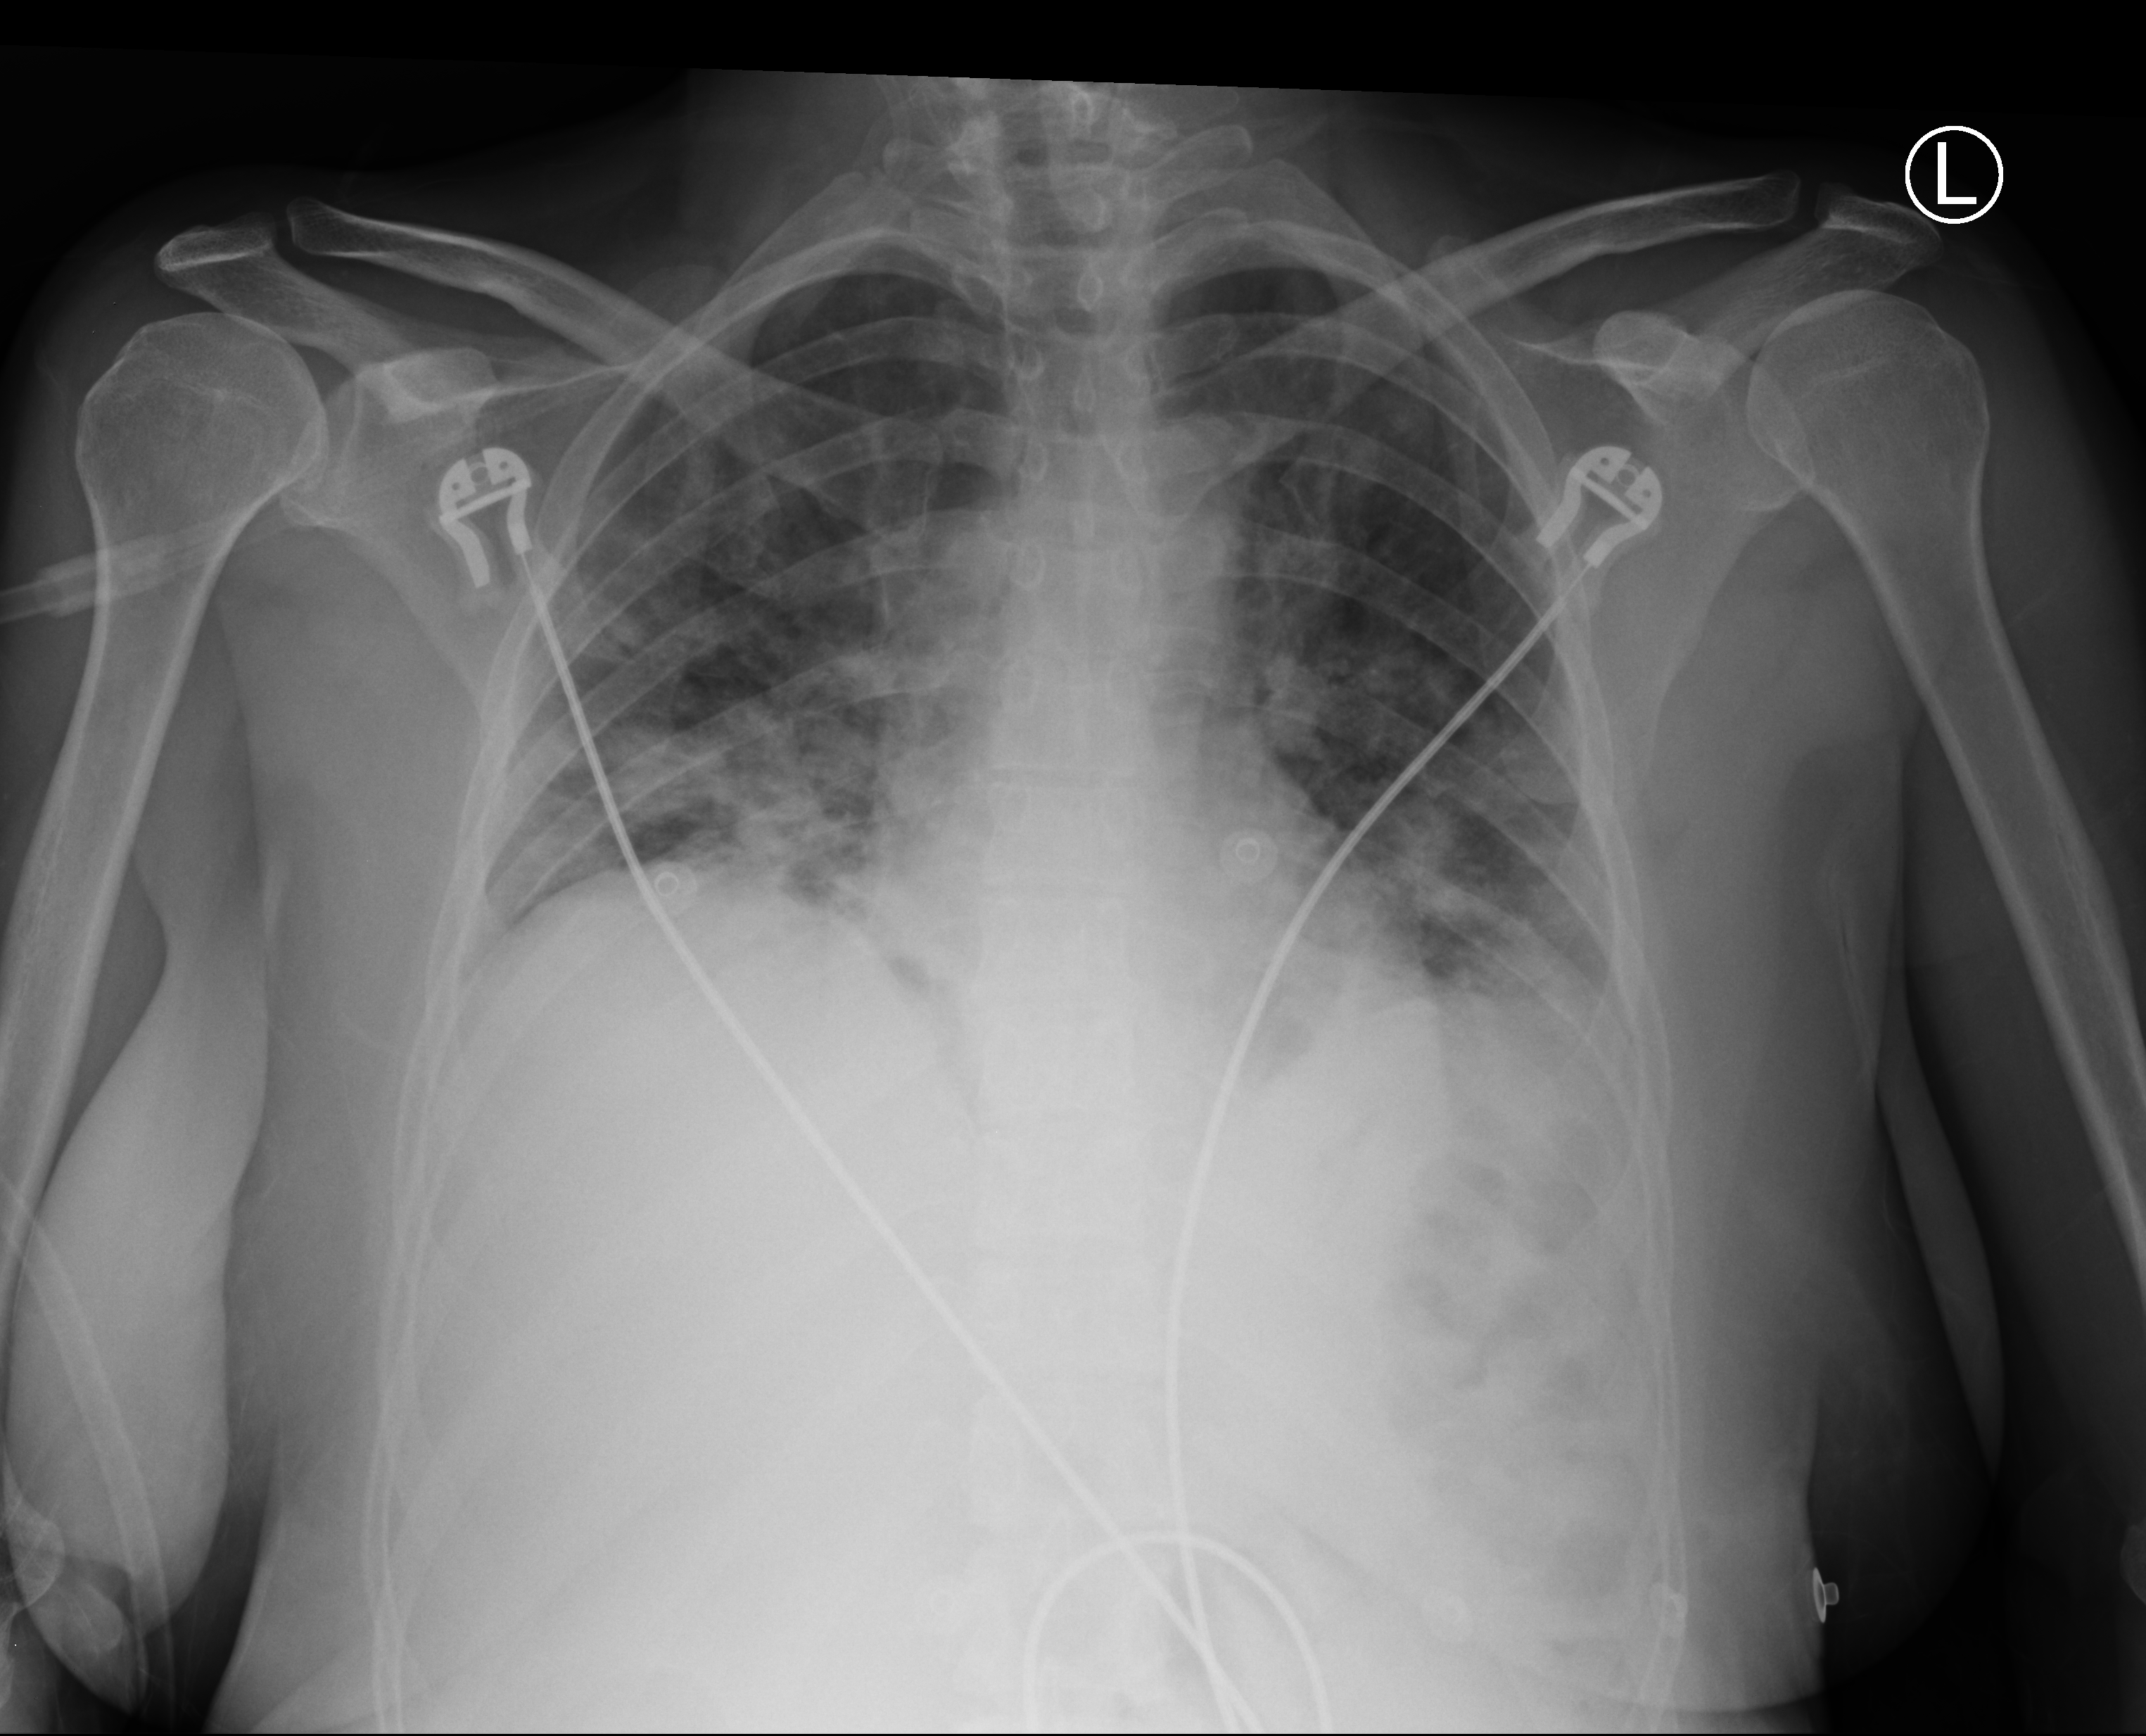
Chest X-ray (portable). Female patient hospitalised with COVID-19, age 18–59 years.
Admission-level facts for this patient (not findings on this image; timing relative to this image not recorded):
- hypertension (admission record): no
- other chronic lung disease (admission record): no
- length of hospital stay: 1 day